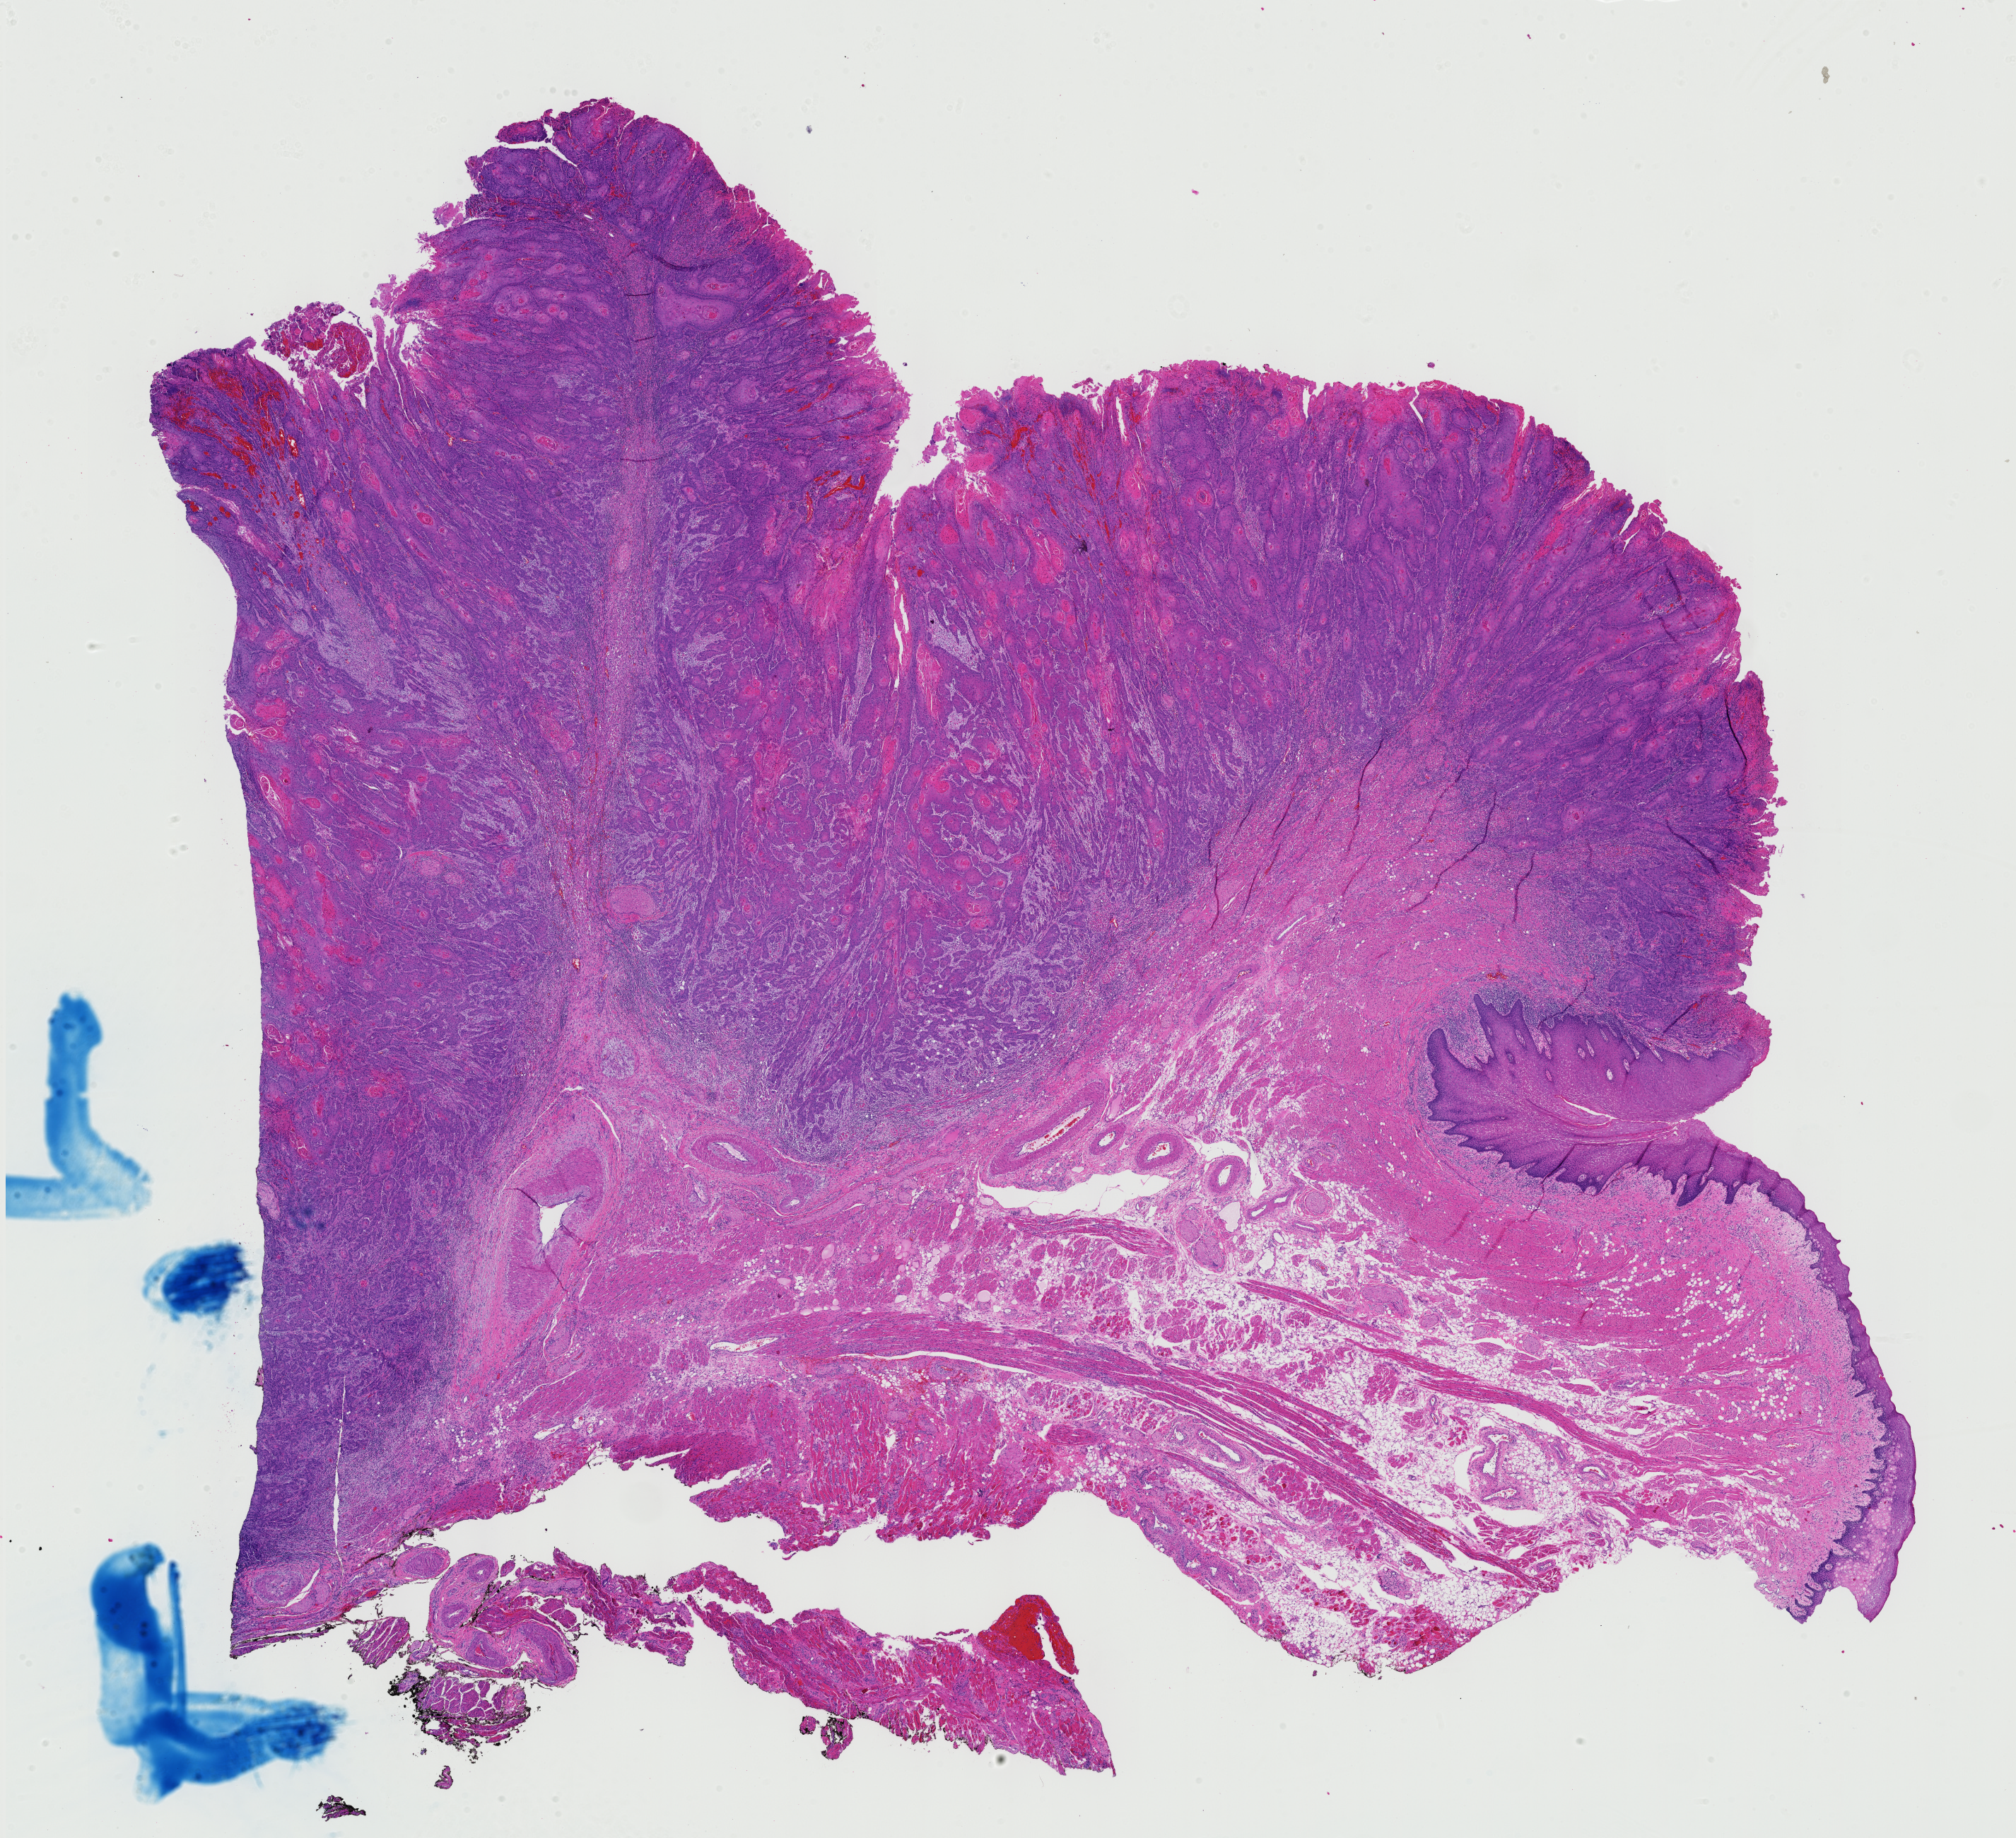
Hematoxylin and eosin (H&E) stained whole-slide image — low-resolution overview of the scanned area, about 20.7 x 18.9 mm (slide scanned at 40x). FFPE section. Head and neck, primary tumour sample. Patient: male, age at initial diagnosis 52 years. Histologic grade: G2 (moderately differentiated).
TNM: T4a N2c M0. Pathologic diagnosis: Squamous cell carcinoma, NOS (floor of mouth, NOS). Lymph nodes positive (case pathology): 4 of 58 examined. AJCC pathologic stage: IVA (7th edition).